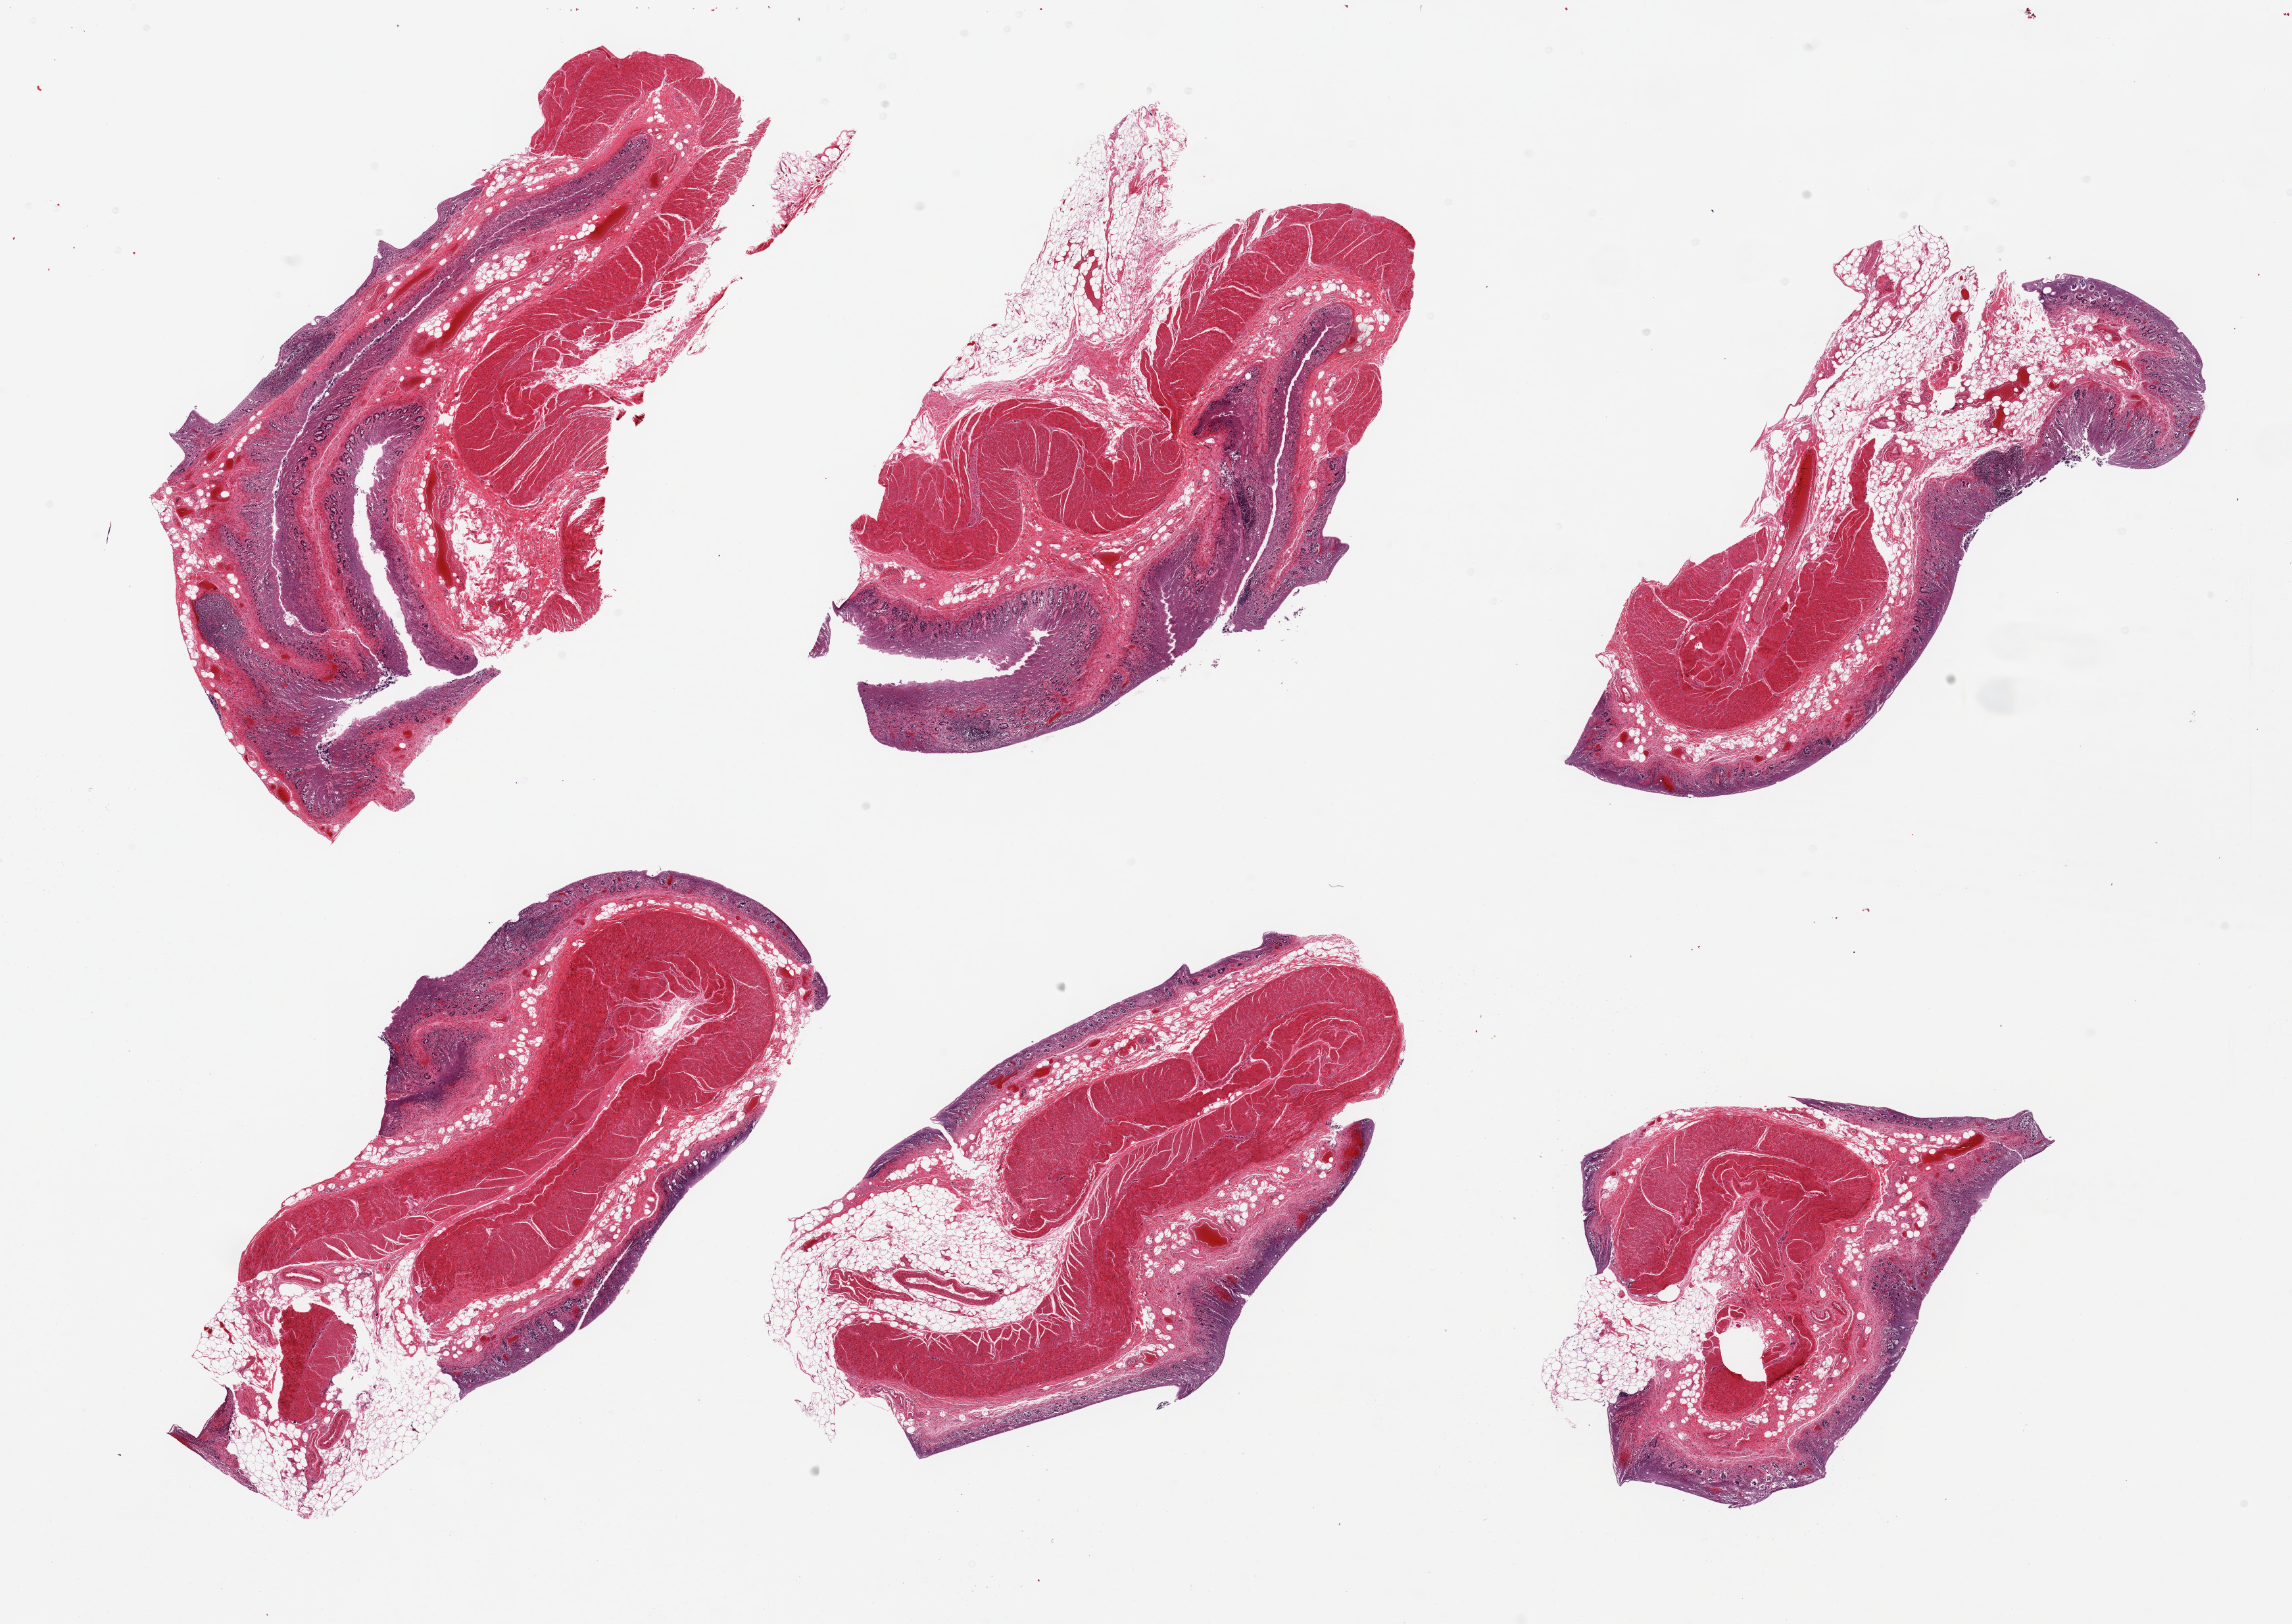
Whole-slide image, H&E stain, brightfield — low-resolution overview of the scanned area, about 27.6 x 19.5 mm (acquisition: 20x scan), PAXgene-fixed, paraffin-embedded tissue, sampled site (target tissue): sigmoid colon, donor tissue sample. Donor sex: male.
Review note (as recorded): 6 pieces; all are full thickness with mucosa.